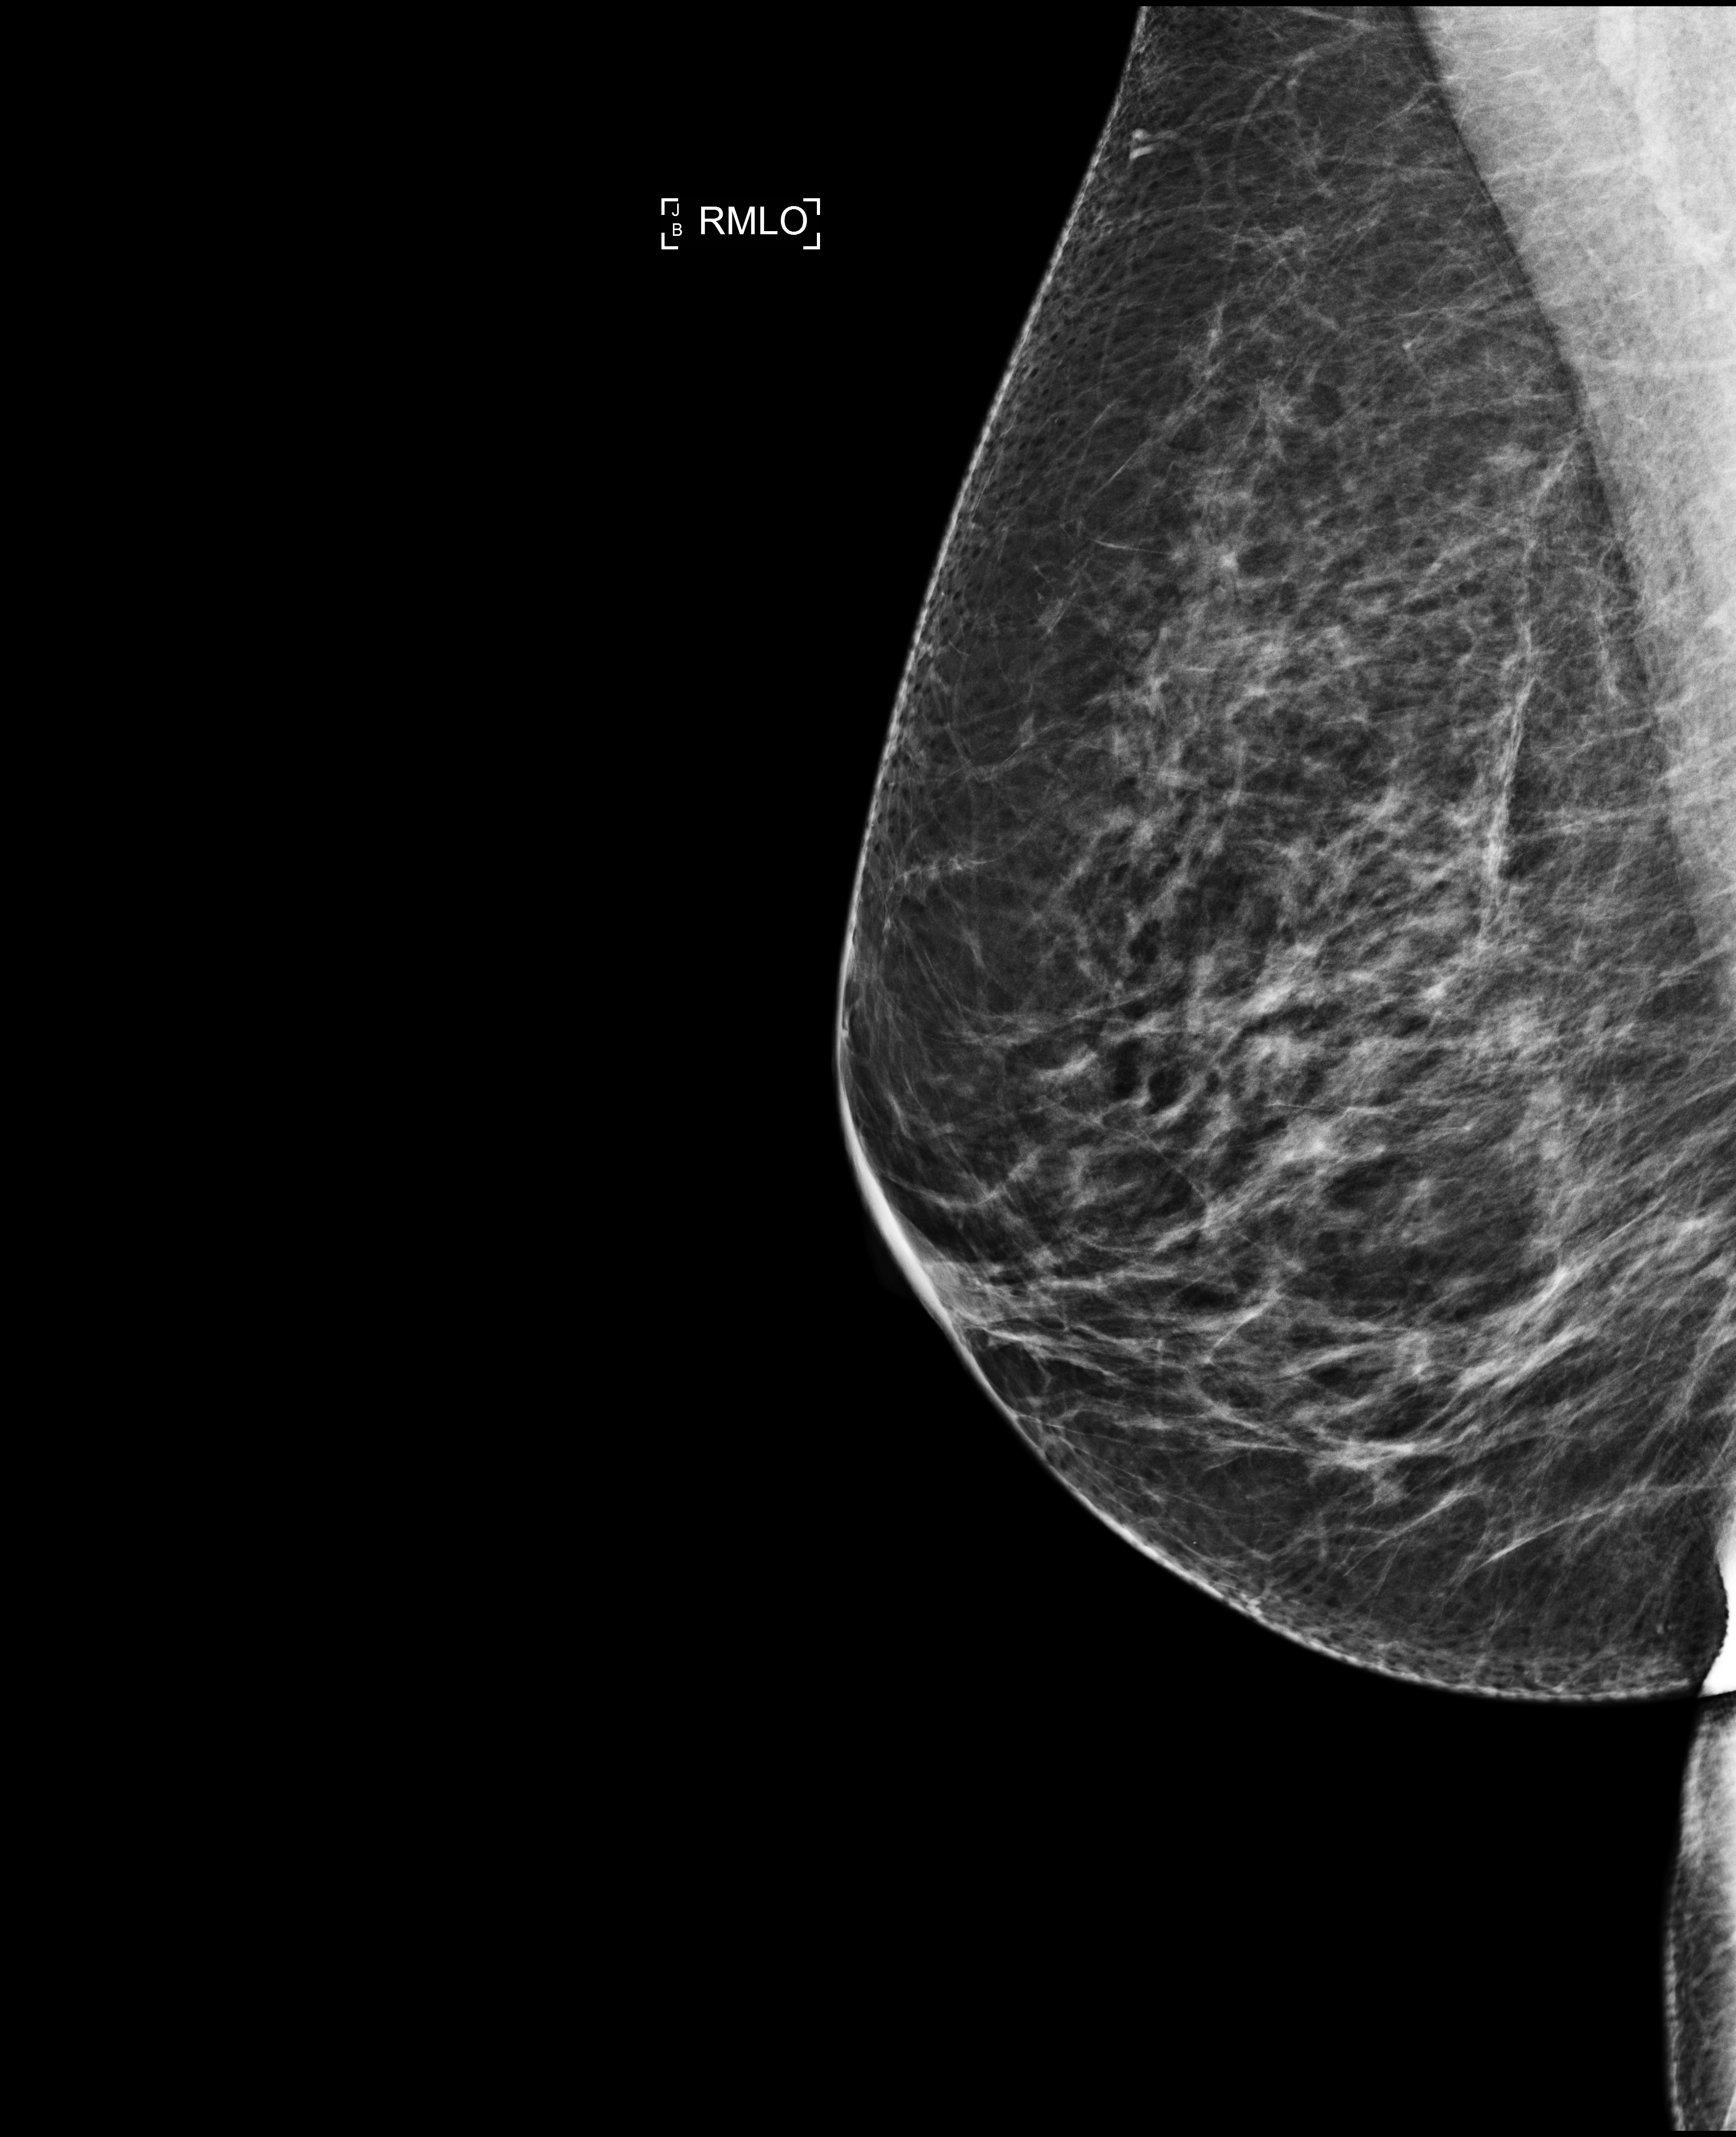
Annual screening mammography examination; compressed breast thickness 71 mm.
Image type: full-field digital mammogram. Breast: right. Projection: medio-lateral oblique projection.